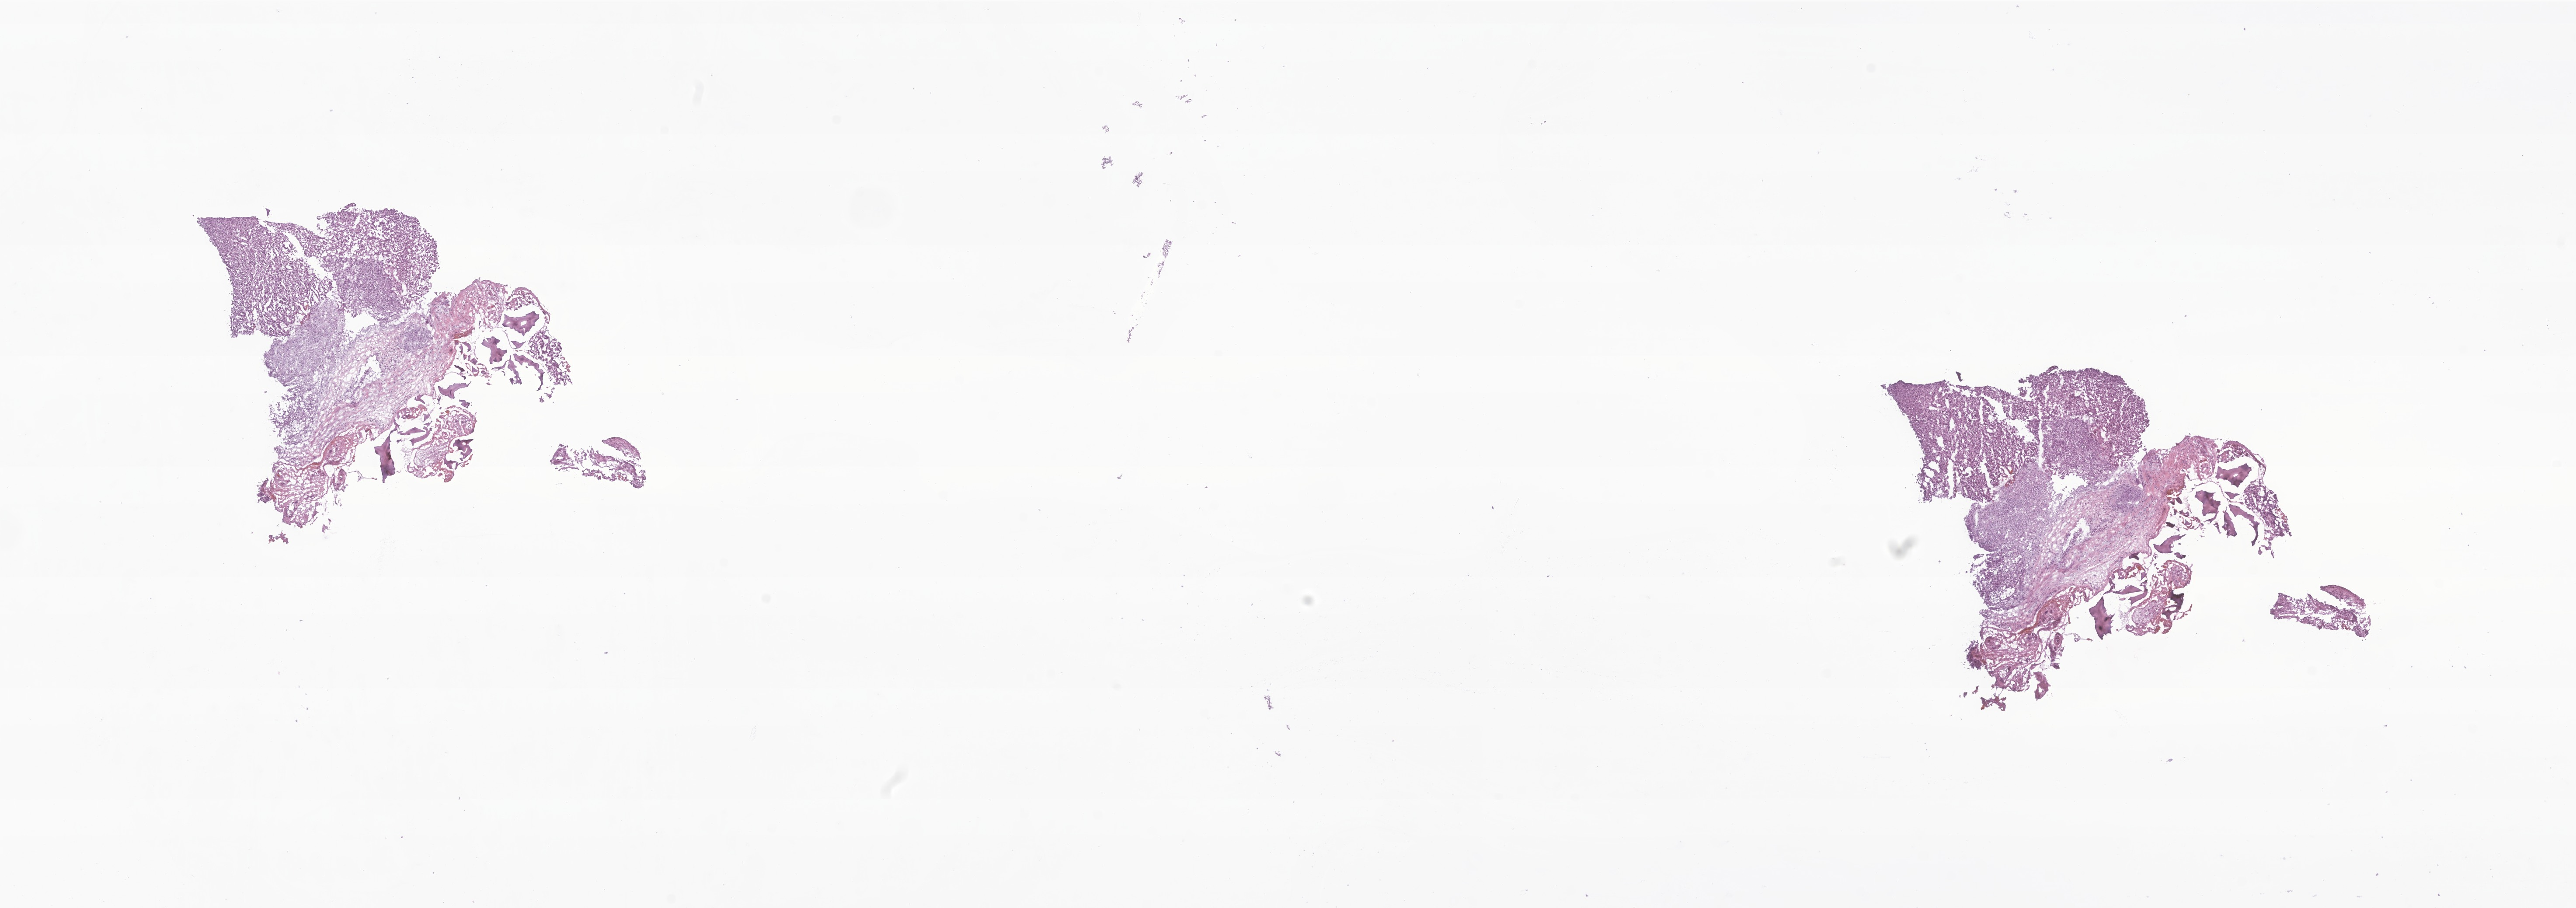
Whole-slide image, H&E stain of tumor tissue from the orbit — whole scanned area (about 24.8 x 8.8 mm) shown as a low-resolution overview; frozen section. Patient: male, age 410 days.
* recorded diagnosis: Alveolar soft part sarcoma